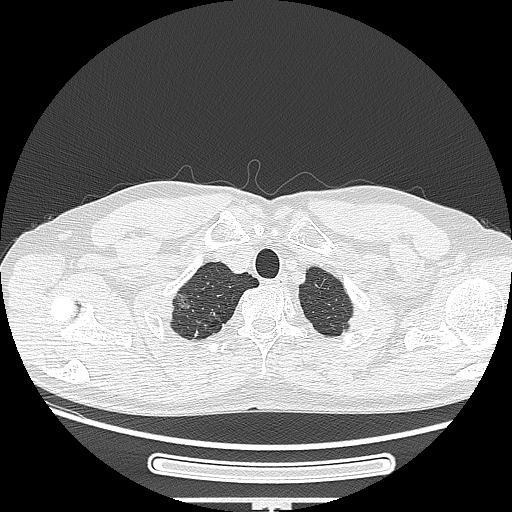
Chest CT, one axial slice; slice 241 of 269 in the series (ordered by position); reconstruction kernel LUNG; 120 kVp; lung window (W 1500 / L -600 HU); 512 × 512 image matrix, field of view 382 × 382 mm. Patient: male, 53 years. From the clinical record (not read from this slice): clinical TNM (as recorded): T1c N0 M0.
Structures marked on this image (bounding box drawn by a radiologist):
- lung tumour (recorded histology: adenocarcinoma): bounding box [x1, y1, x2, y2] px = [167, 287, 192, 324]